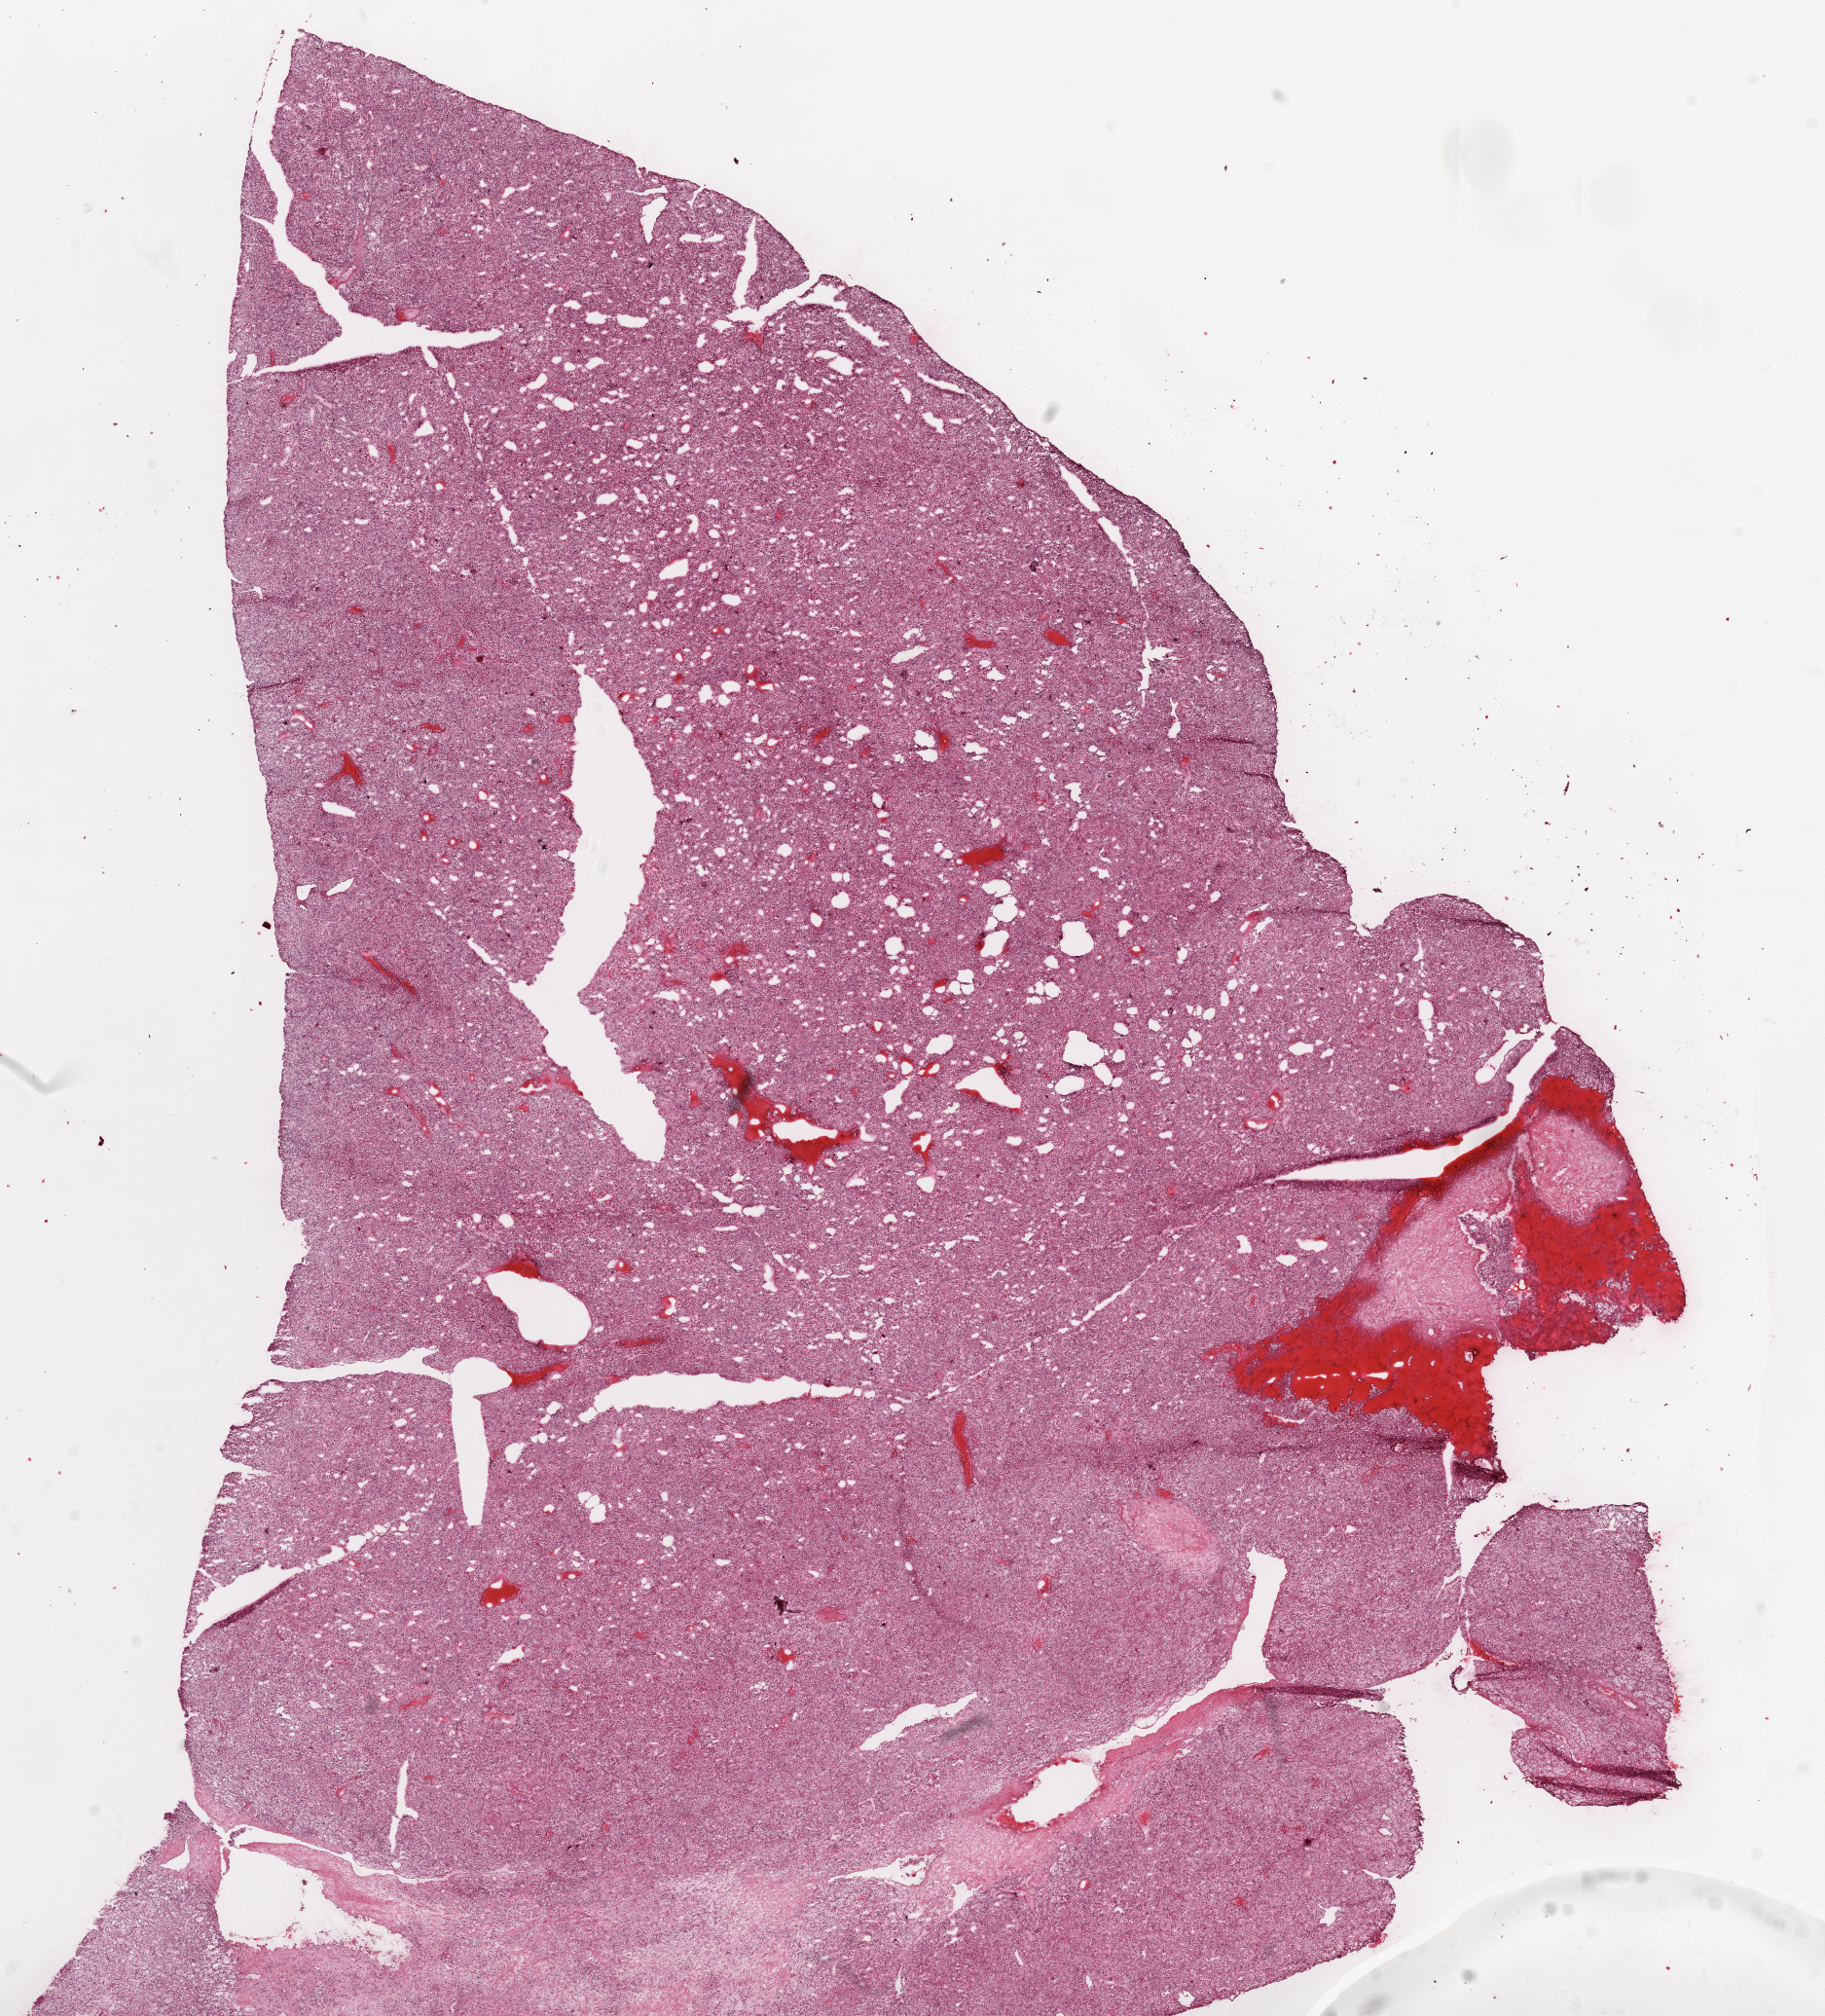
H&E whole-slide image, whole scanned area (about 15.0 x 16.6 mm, acquisition: 20x scan) shown as a low-resolution overview, frozen section from the top of the tissue portion, primary tumour sample from the kidney. Female patient; age at initial diagnosis 70 years. Histologic grade: G2 (moderately differentiated). Pathologist review of this section (percent, as recorded): tumour cells 95%, tumour nuclei 85%, normal cells 0%, stromal cells 5%, necrosis 0%.
Histologic diagnosis: Clear cell adenocarcinoma, NOS. Laterality: right. AJCC pathologic stage: I.